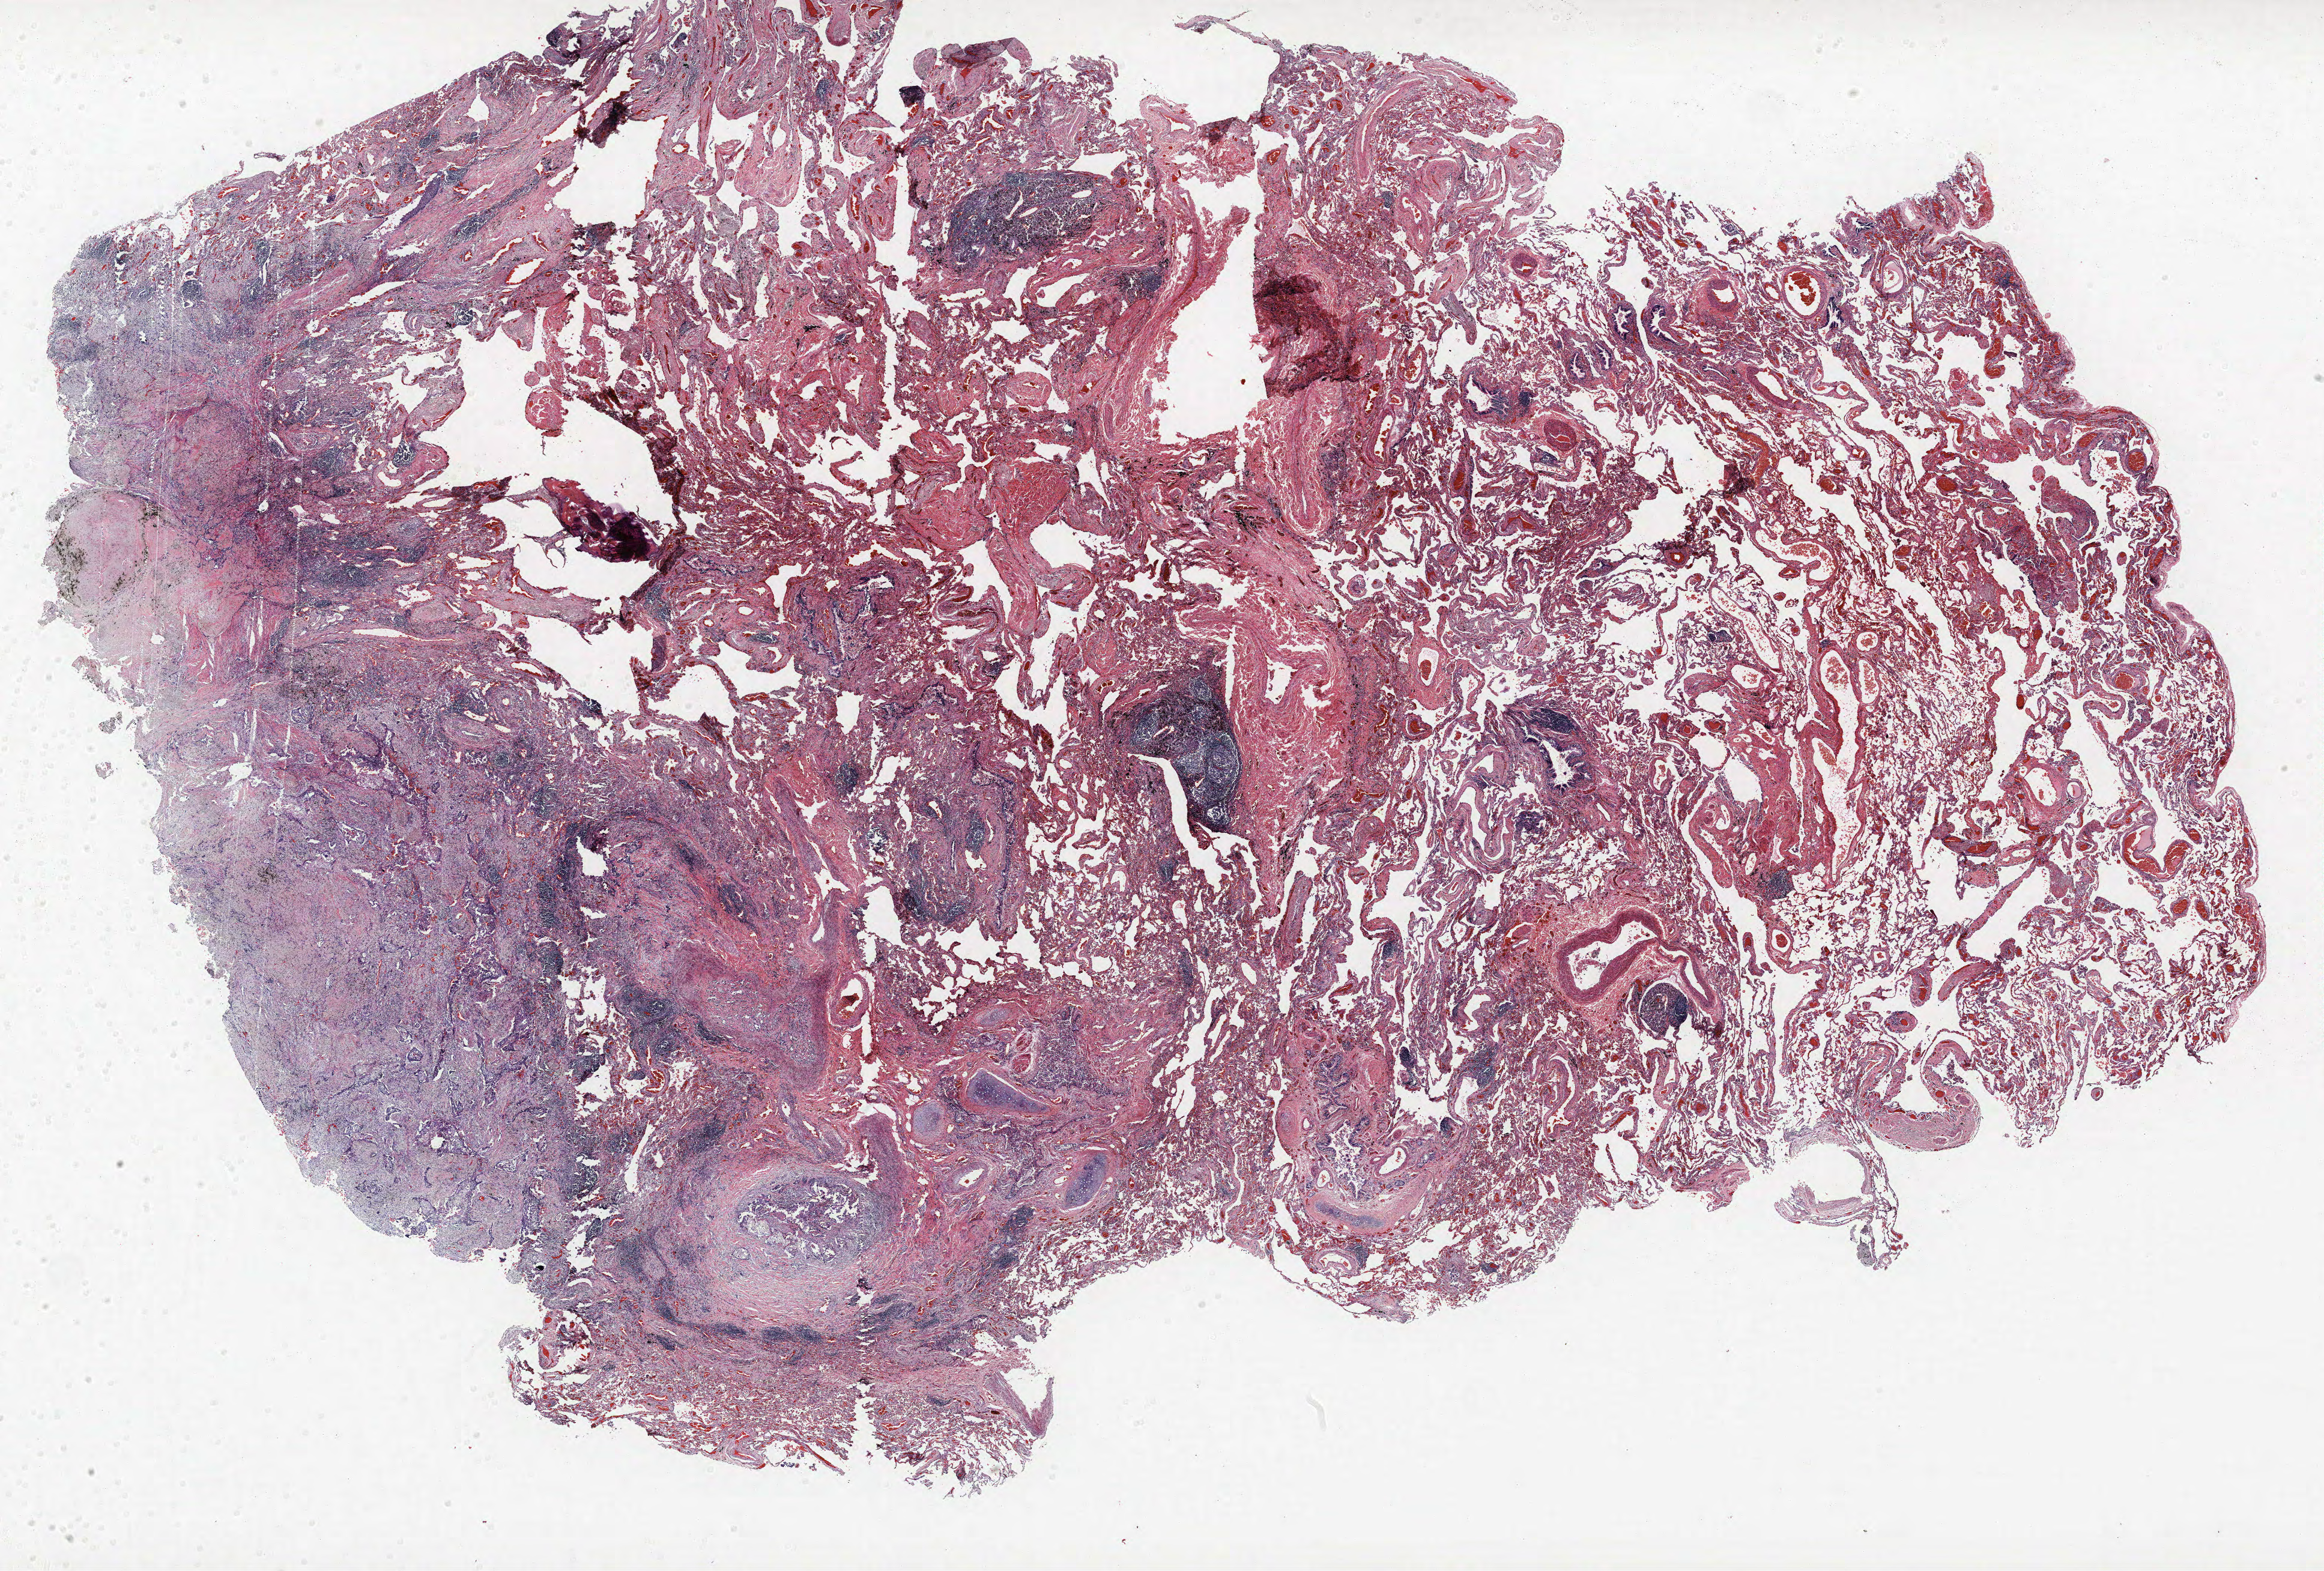
Whole-slide histology image, H&E-stained — a low-resolution overview of the entire scanned area, about 31.0 x 20.9 mm. Formalin-fixed paraffin-embedded (FFPE) section. Lung tissue. Male, age 59 at enrolment. Current smoker at enrolment. Grade: moderately differentiated (G2).
Tumour size (pathology): 30 mm. Participant's lung-cancer diagnosis: Squamous cell carcinoma, NOS. Primary tumour location (clinical record): right upper lobe. Stage (AJCC 6th edition): IA.